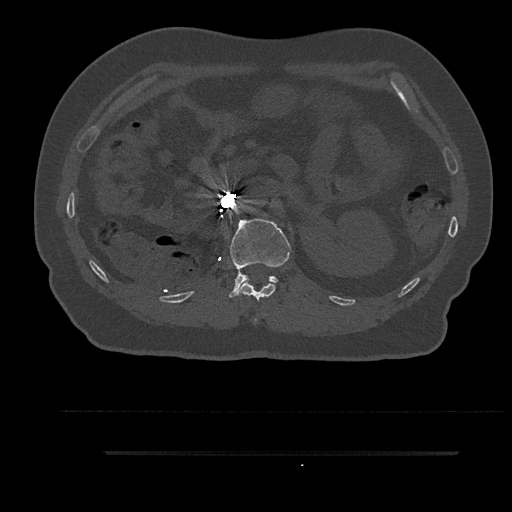
CT including the spine, one axial slice; position 201 of 797 along the scan axis; reconstruction kernel Br40s/3; 120 kVp; bone window (W 1800 / L 400 HU); 0.5 mm slice thickness; 512 × 512 image matrix, field of view 432 × 432 mm. Patient: male, 63 years. From the clinical record (not read from this slice): primary cancer: renal.
Annotated regions visible in this slice (semi-automatically segmented with operator editing):
- L1 vertebra: bounding box (x1, y1, x2, y2) in pixels: (229, 219, 291, 298)
- T12 vertebra: (239, 281, 276, 322)